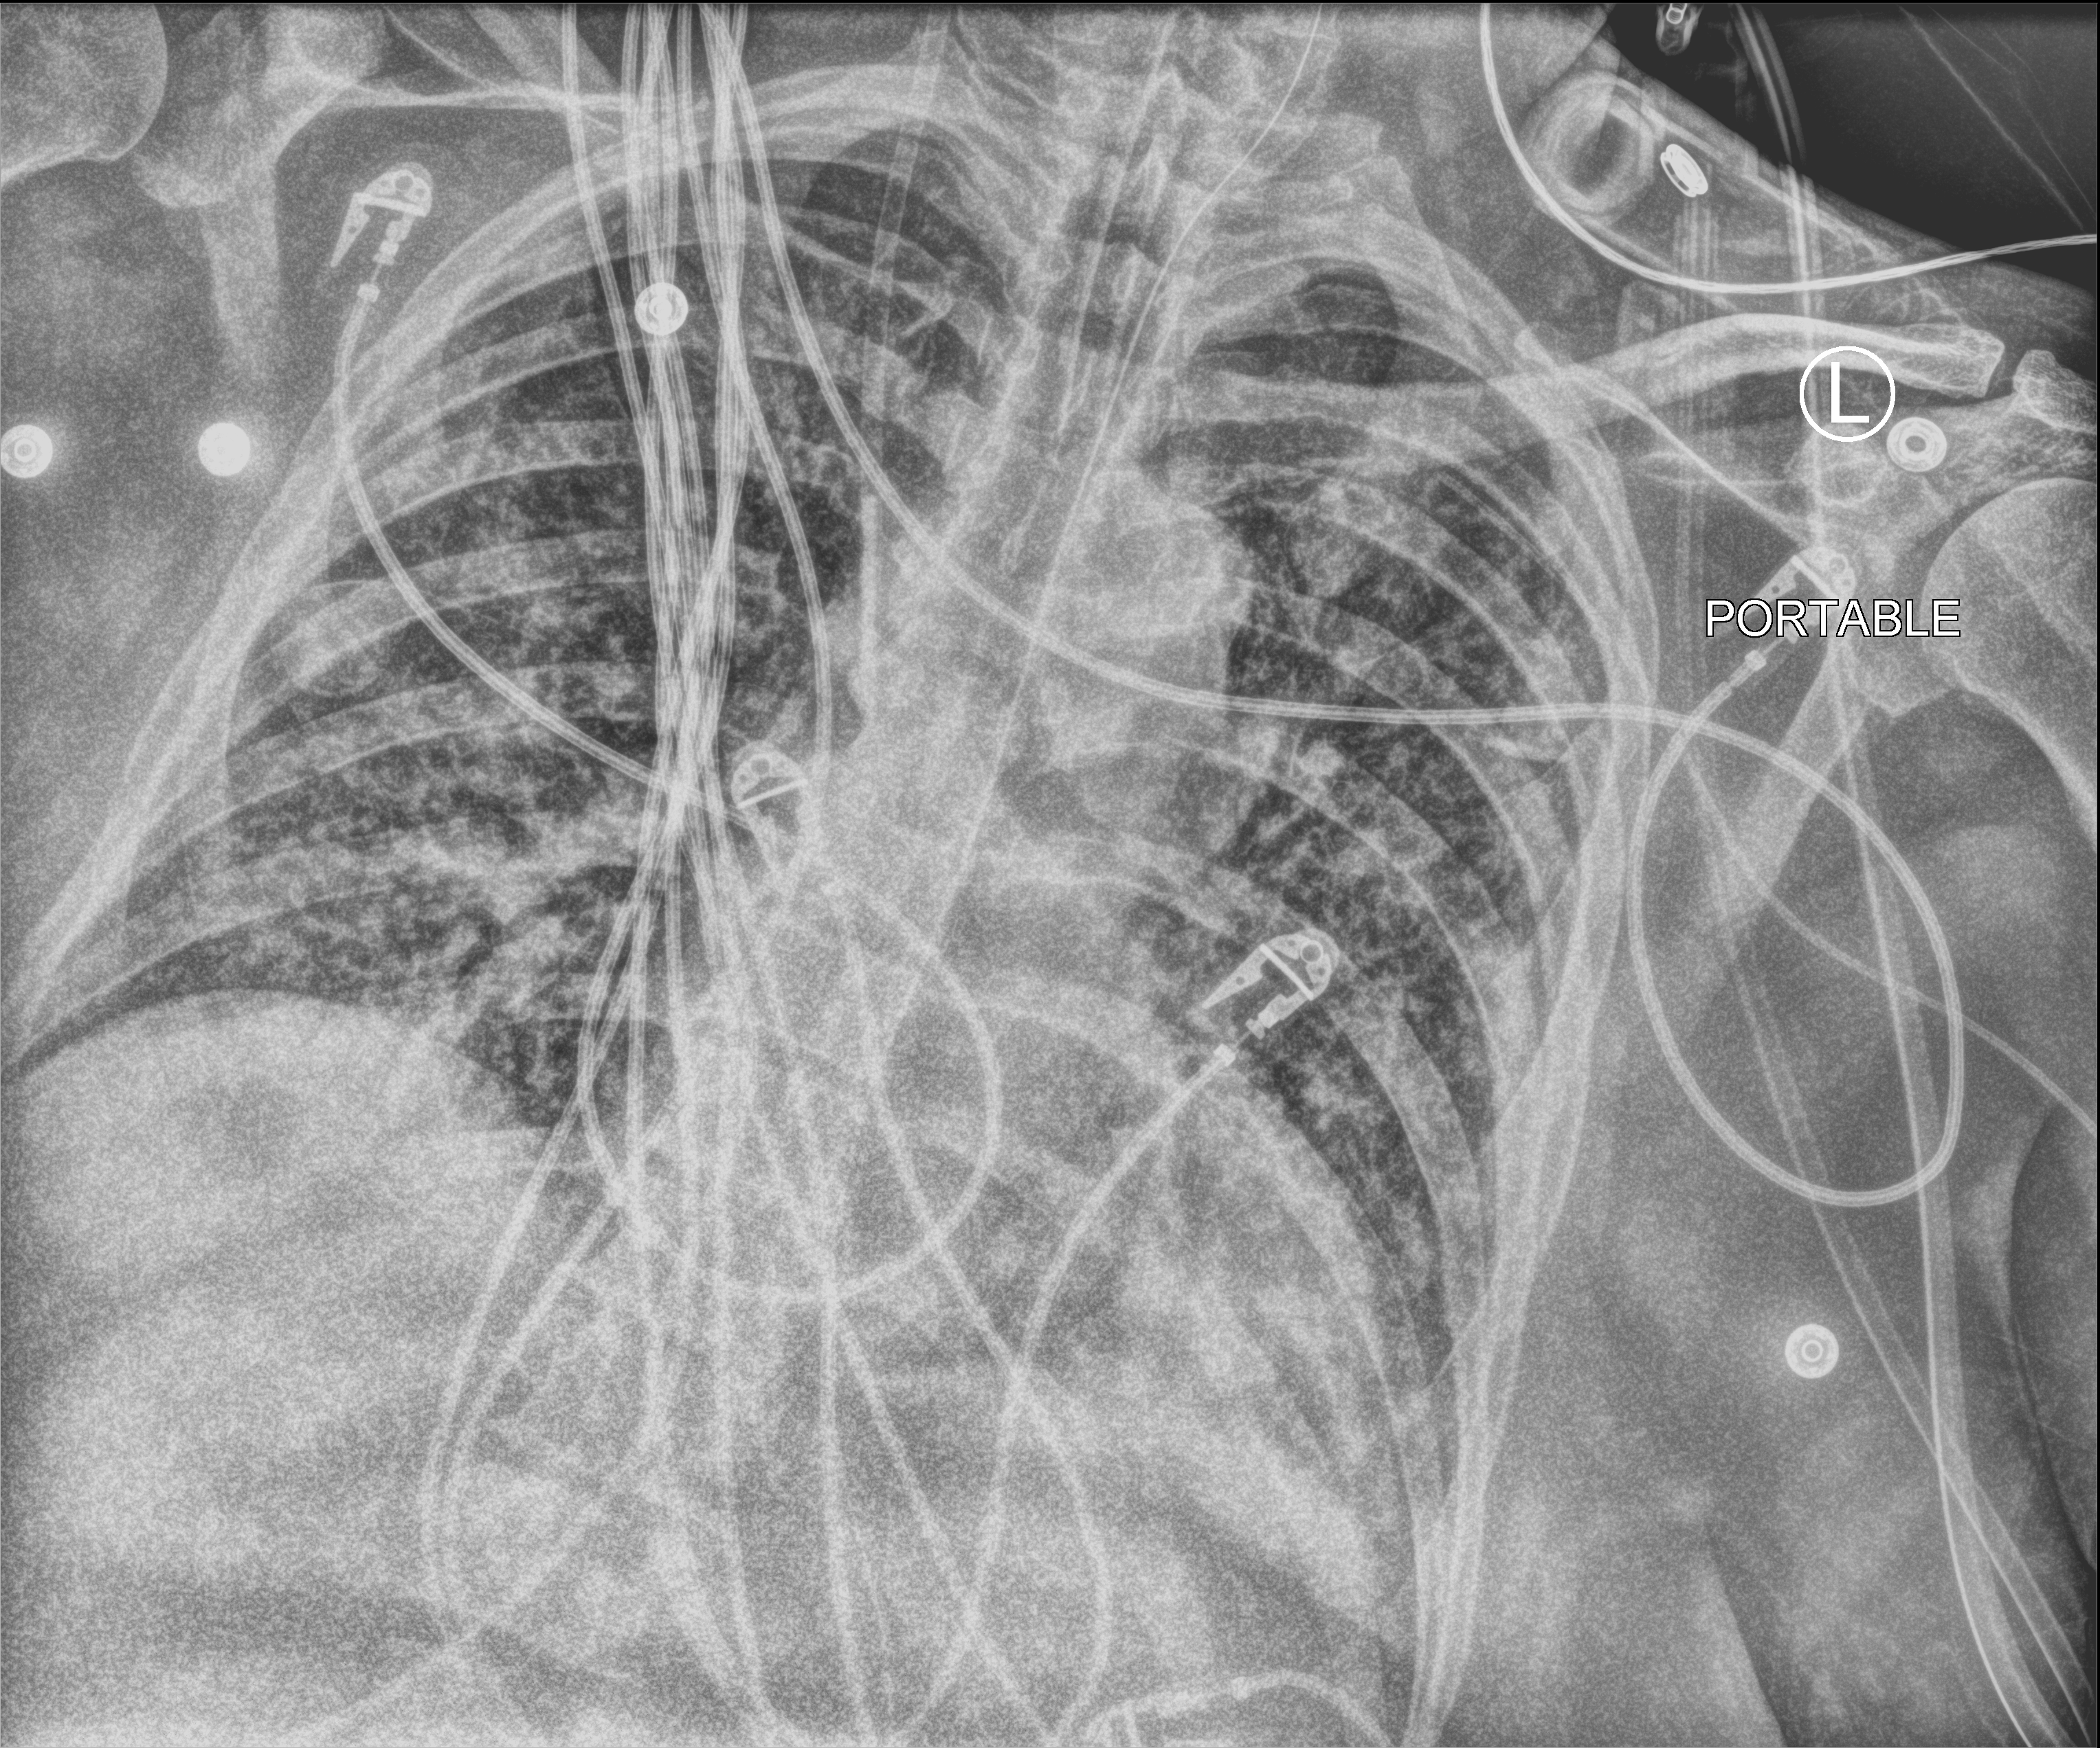
Chest X-ray (portable). Patient hospitalised with COVID-19; male, aged 60–74 years.
Admission-level facts for this patient (not findings on this image; timing relative to this image not recorded): COPD (admission record): no; mechanically ventilated during this hospital stay: yes; admitted to intensive care during this hospital stay: yes.